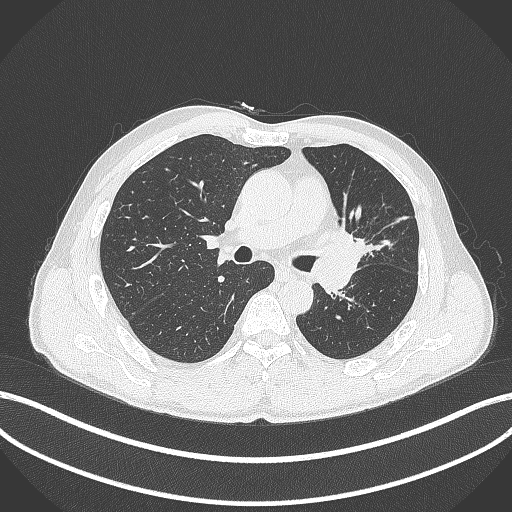
Chest CT, one axial slice; lung window (W 1500 / L -600 HU); 512 × 512 image matrix, field of view 400 × 400 mm. Patient: male, 57 years. From the clinical record (not read from this slice): clinical TNM (as recorded): T2b N0 M0.
Outlined on this slice (rectangle marked by the reading radiologist):
- lung tumour (recorded histology: squamous cell carcinoma): bounding box [x1, y1, x2, y2] px = [318, 229, 369, 267]